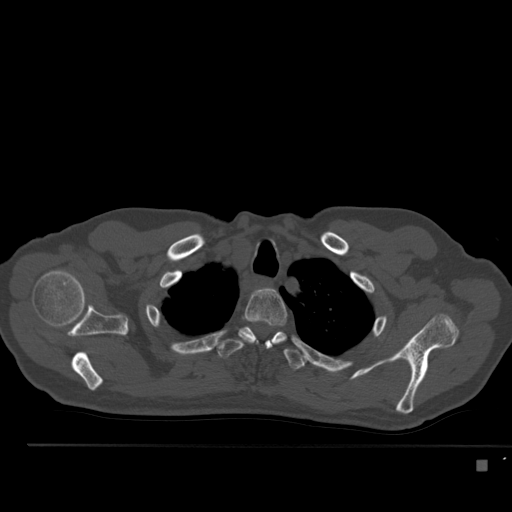
CT including the spine, one axial slice. Position 406 of 517 along the scan axis. 120 kVp. Bone window (W 1800 / L 400 HU). 1.5 mm slice thickness. 512 × 512 image matrix. Male patient, age 70 years. Case-level facts recorded for this patient, not image findings: primary cancer: renal.
Structures marked on this image (semi-automatic segmentation, software-assisted and operator-edited):
- T2 vertebra: bounding box <239,289,288,345> (left, top, right, bottom; pixels)
- T3 vertebra: <216,326,306,370>